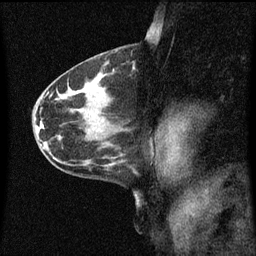
Breast MRI (dynamic contrast-enhanced), one sagittal slice; slice 34 of 60 in the series (ordered by position); dynamic contrast-enhanced series, image 2 of 3 at this slice position (ordered by acquisition); 1.5 T; TE 4.2 ms, TR 8.4 ms; 2 mm slice thickness; 256 × 256 image matrix, field of view 200 × 200 mm. Female patient, age 41 years.
Outlined on this slice (semi-automatic segmentation, software-assisted and operator-edited):
- analysis volume of interest (the breast-tissue region the enhancement analysis was run in; not a lesion): bounding box [x1, y1, x2, y2] px = [121, 58, 139, 83]
- tumour enhancement mask (voxels above the 70 % enhancement threshold inside the analysis volume of interest): [131, 68, 136, 77]